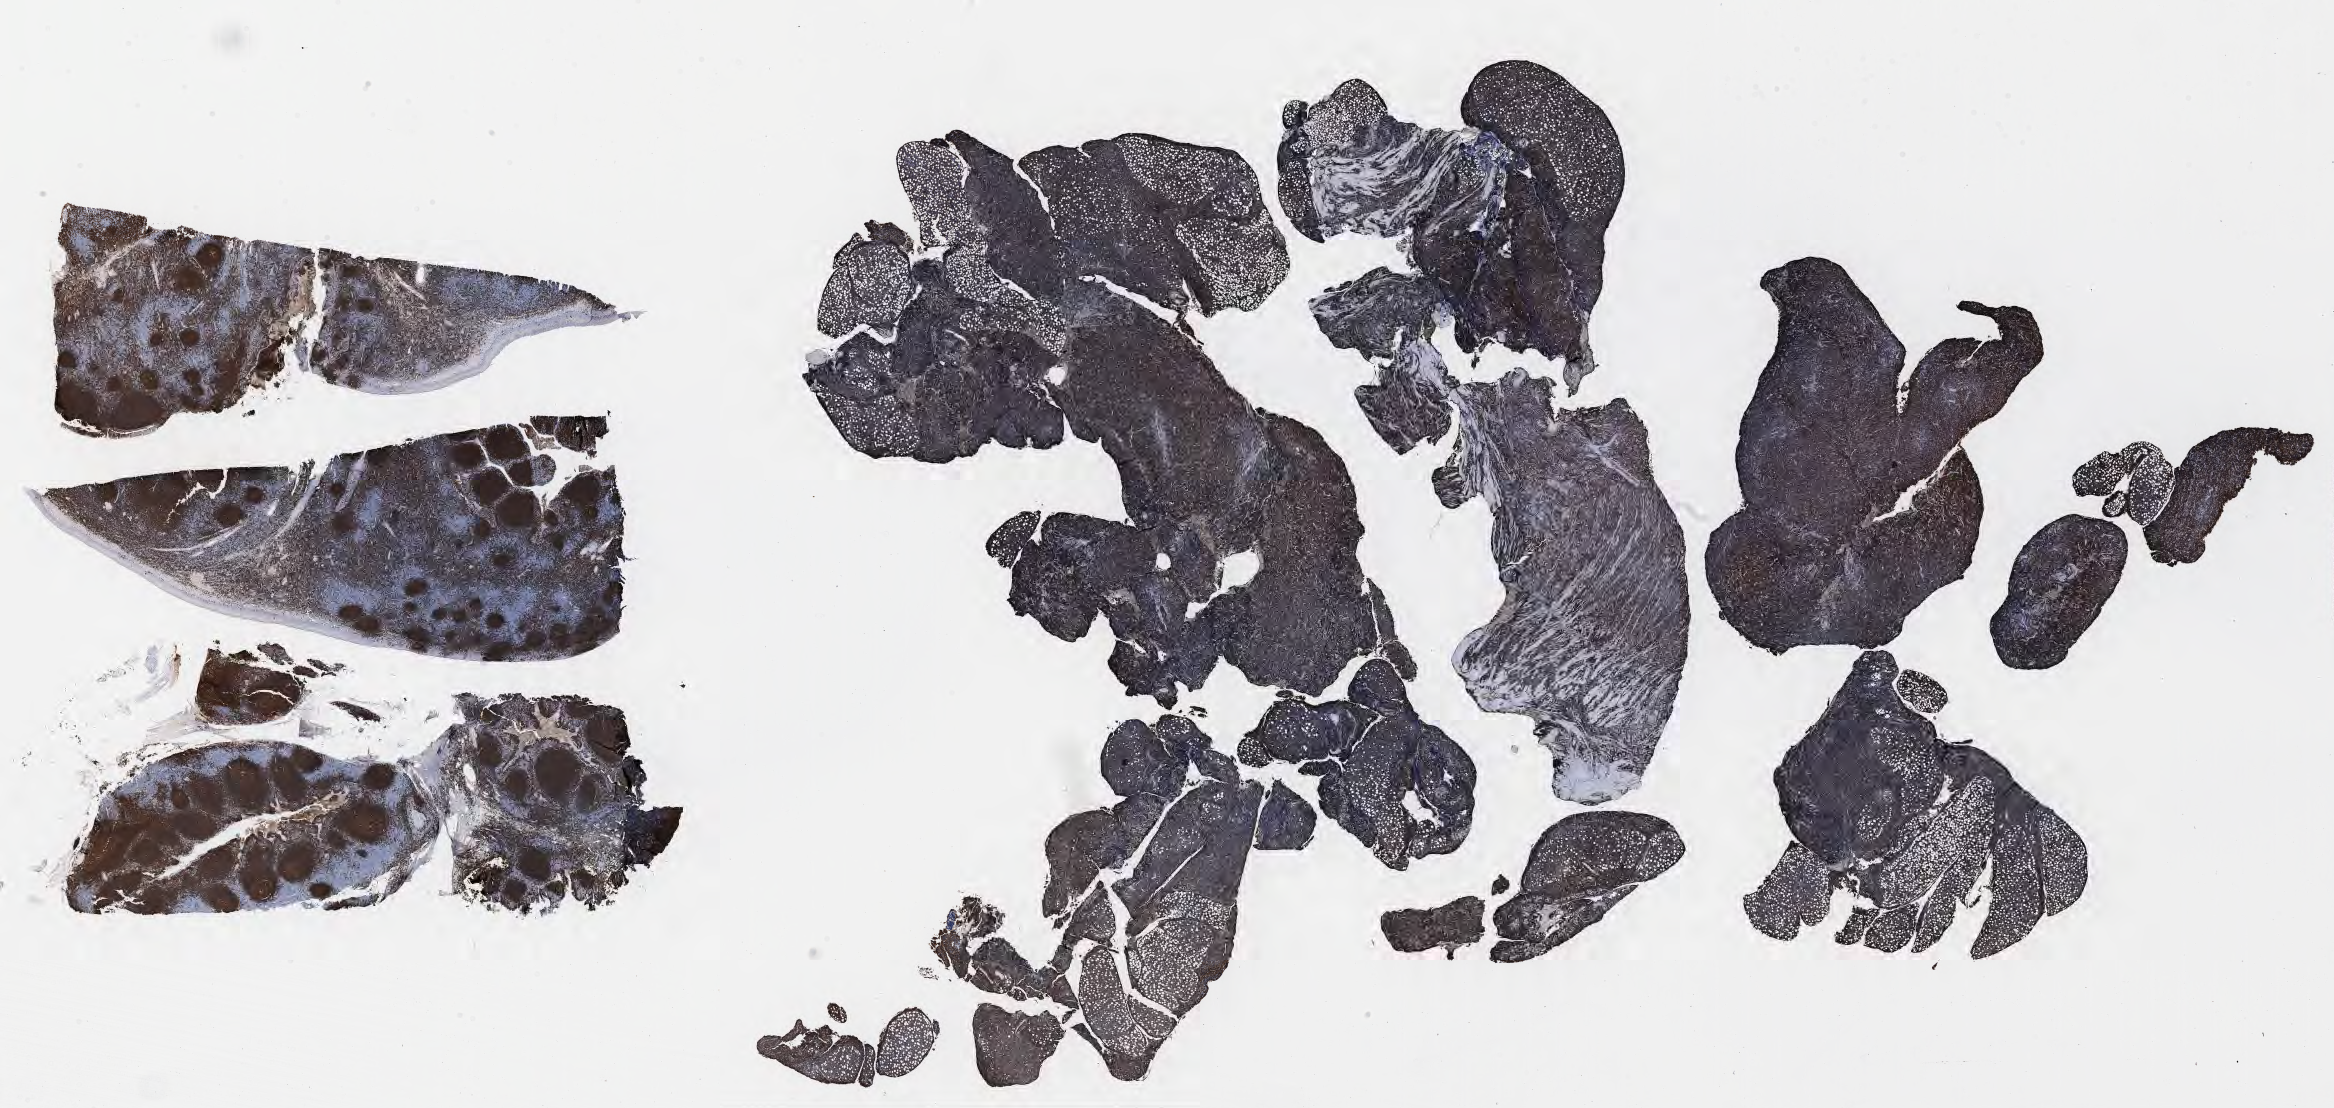
Immunohistochemistry (IHC) whole-slide image stained for CD20 — whole scanned area (about 37.7 x 17.9 mm) shown as a low-resolution overview, tumor tissue, anatomic site: abdomen proper. Patient: male, age at initial diagnosis 4 years.
Histologic diagnosis: Burkitt lymphoma, NOS.